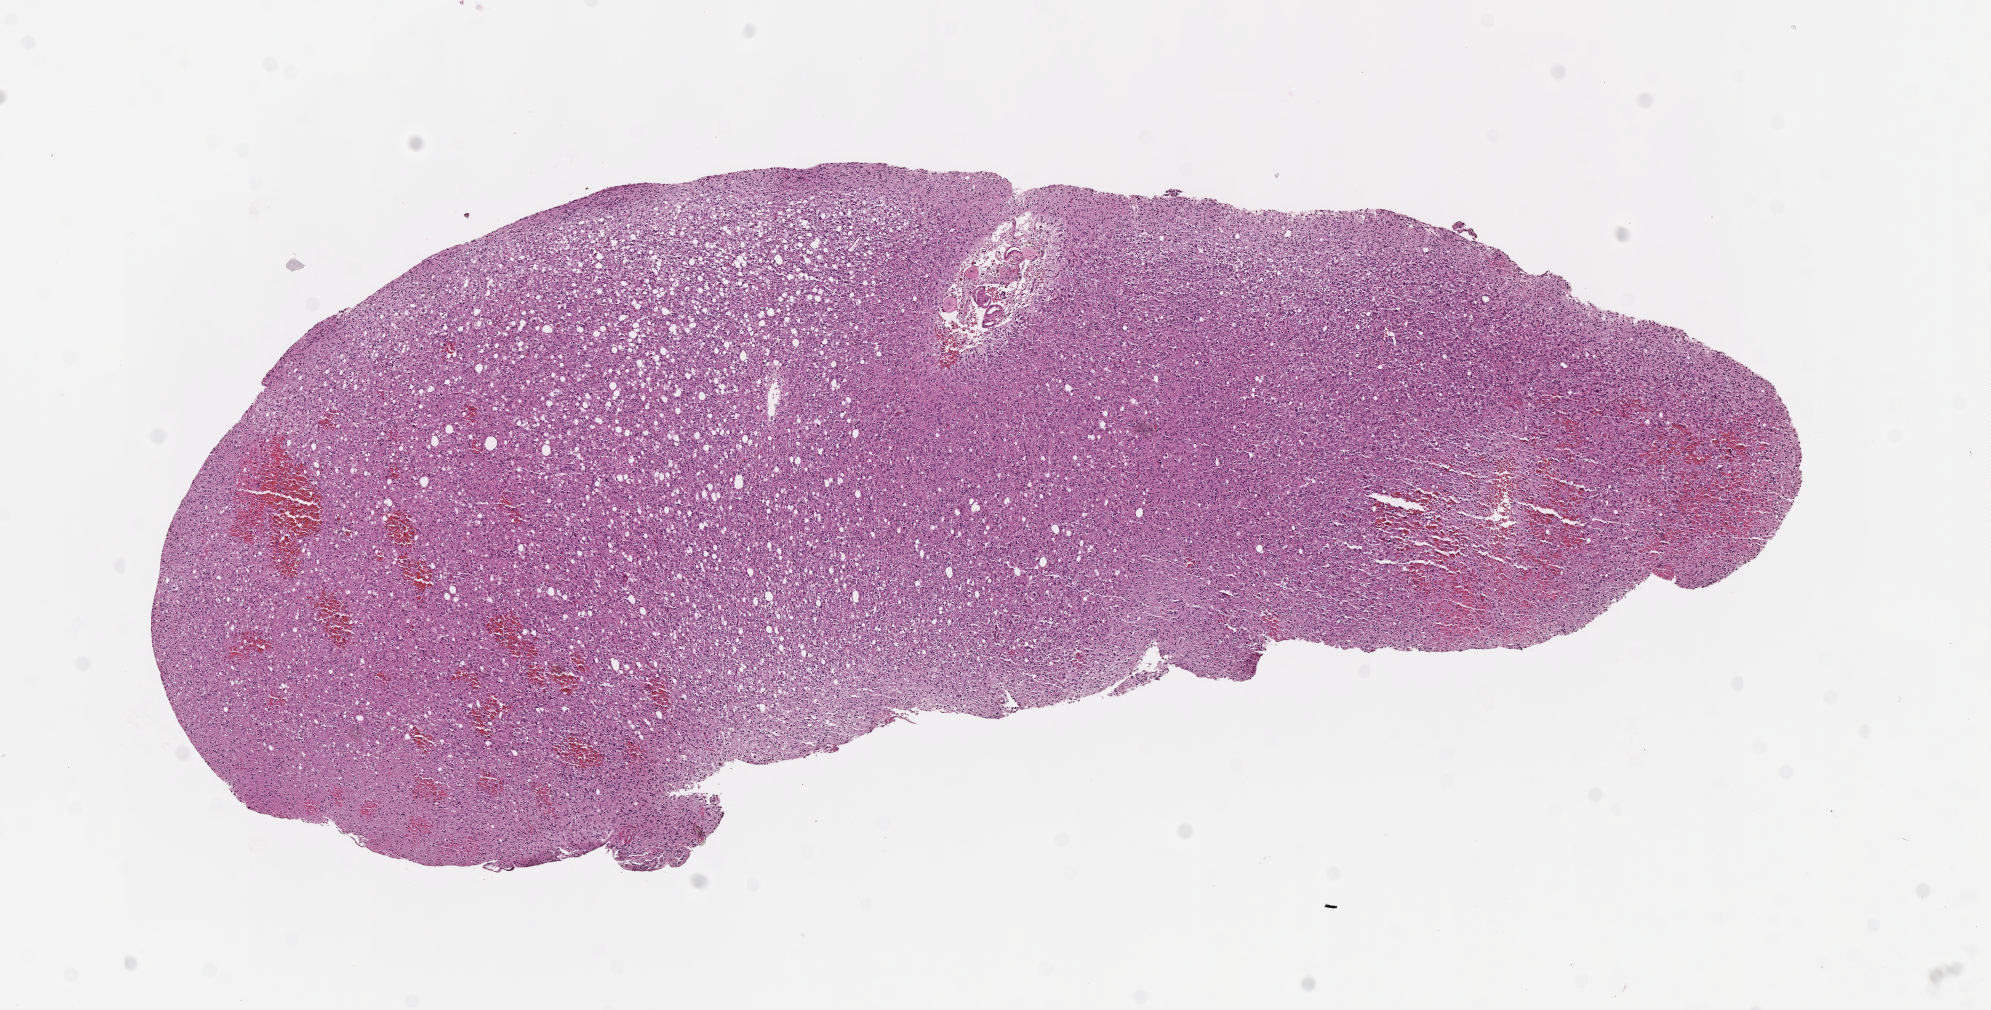
Hematoxylin and eosin (H&E) stained whole-slide image, a low-resolution overview of the entire scanned area, about 8.1 x 4.1 mm (slide scanned at 40x); formalin-fixed paraffin-embedded (FFPE) diagnostic section; sample: primary tumour, brain. Female, age 46 years at initial diagnosis. Histologic grade: G3 (poorly differentiated).
Diagnosis: Astrocytoma, anaplastic (cerebrum).